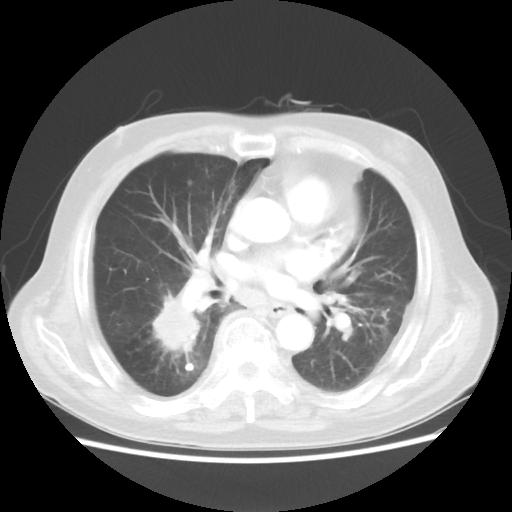
Chest CT, one axial slice. Slice 19 of 44 in the series (ordered by position). Lung window (W 1500 / L -600 HU). 512 × 512 image matrix, field of view 359 × 359 mm. Patient: male, 83 years. Case-level facts recorded for this patient, not image findings: clinical TNM (as recorded): T2 N3 M0.
Outlined on this slice (bounding box drawn by a radiologist):
- lung tumour (recorded histology: adenocarcinoma): bounding box <142,292,206,374> (left, top, right, bottom; pixels)